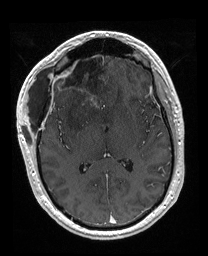
Brain MRI from a brain-tumour surgery series, one axial slice. Slice 93 of 176 in the series (ordered by position). T1-weighted post-contrast. 1 mm slice thickness. 208 × 256 image matrix. From the clinical record (not read from this slice): histopathology: Astrocytoma; WHO grade: 4; IDH mutation: yes; tumour location: Right Orbitofrontal Anterior Temporal Insular.
Structures marked on this image (outlined manually by an expert reader):
- previous resection cavity: bounding box <56,52,106,111> (left, top, right, bottom; pixels)